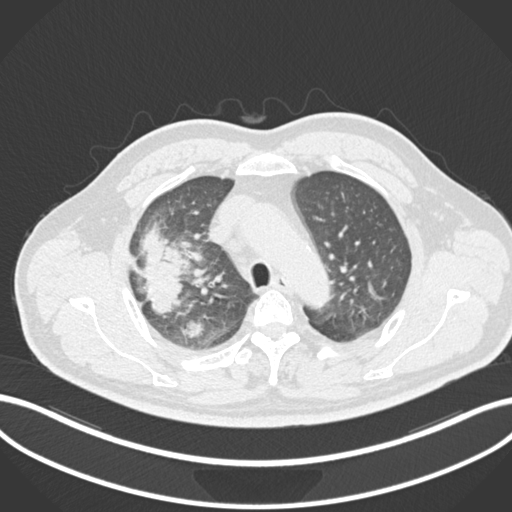
Chest CT, one axial slice; reconstruction kernel B30f; lung window (W 1500 / L -600 HU); 1 mm slice thickness; 512 × 512 image matrix. Patient: male, 55 years. Case-level facts recorded for this patient, not image findings: clinical TNM (as recorded): T3 N2 M1.
Outlined on this slice (bounding box drawn by a radiologist):
- lung tumour (recorded histology: adenocarcinoma): bounding box <134,214,193,320> (left, top, right, bottom; pixels)